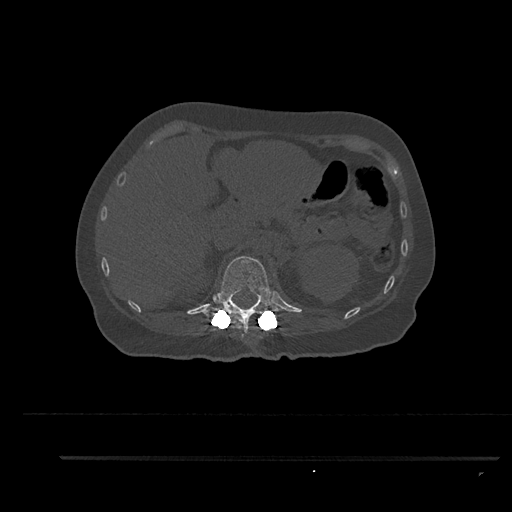
CT including the spine, one axial slice; position 261 of 797 along the scan axis; reconstruction kernel Br40s/3; 120 kVp; bone window (W 1800 / L 400 HU); 0.5 mm slice thickness; 512 × 512 image matrix, field of view 408 × 408 mm. Female patient, age 44 years. Case-level facts recorded for this patient, not image findings: primary cancer: renal.
Outlined on this slice (semi-automatic segmentation, software-assisted and operator-edited):
- T12 vertebra: bounding box <205,256,282,338> (left, top, right, bottom; pixels)